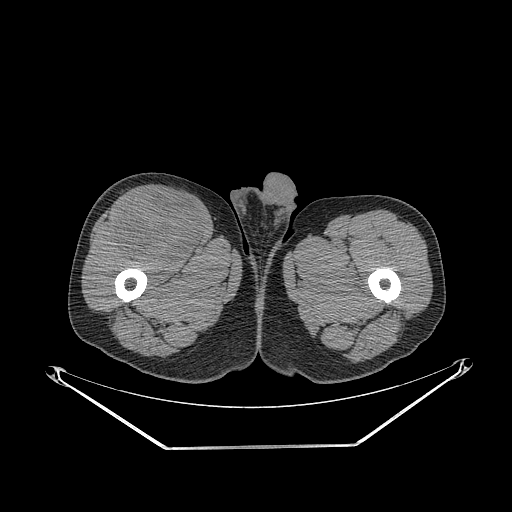
CT of an extremity soft-tissue mass (from a PET/CT study), one axial slice; slice 287 of 311 in the series (ordered by position); reconstruction kernel STANDARD; 140 kVp; soft-tissue window (W 400 / L 40 HU); 512 × 512 image matrix, field of view 500 × 500 mm. Male patient. From the clinical record (not read from this slice): histological type: pleiomorphic leiomyosarcoma; grade: intermediate; site of the primary tumour: right thigh.
Structures marked on this image (expert contour drawn on MRI and transferred to this co-registered scan by the dataset authors):
- gross tumour volume including surrounding oedema: box from (x=112, y=192) to (x=204, y=263) px
- gross tumour volume (mass): (x=114, y=192)–(x=204, y=263)